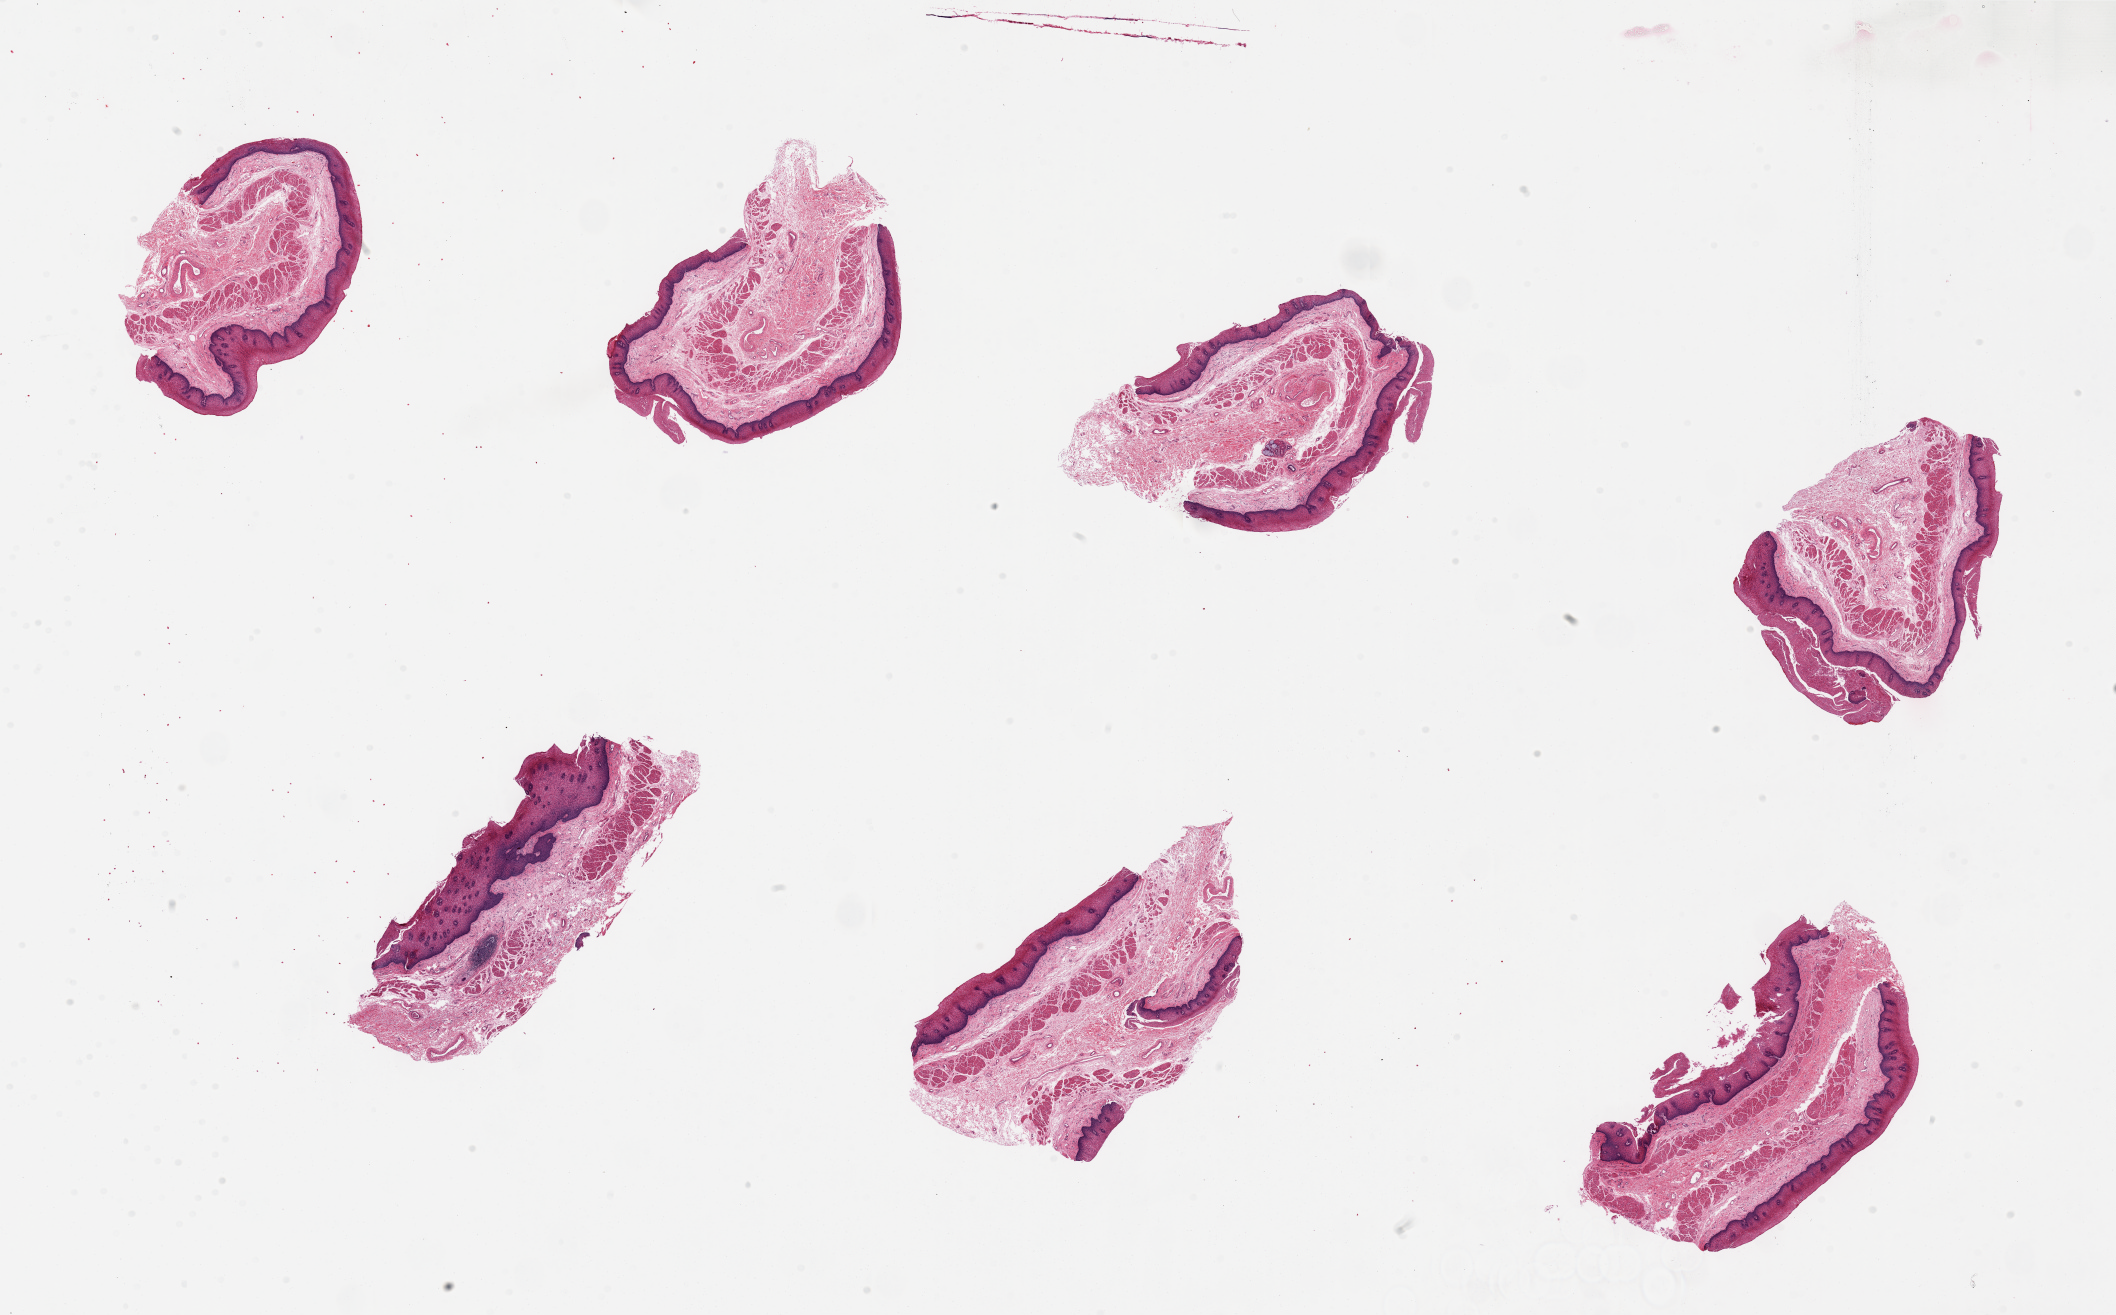
Whole-slide image, haematoxylin and eosin stain, shown as a low-resolution overview of the whole scanned area (about 33.5 x 20.8 mm). PAXgene-fixed, paraffin-embedded tissue. Sampled site (target tissue): esophageal mucous membrane. Tissue donor sample. Donor: male.
Pathologist's review note for this sample: 7 pieces, includes few submucosal glands with oncocytic change.